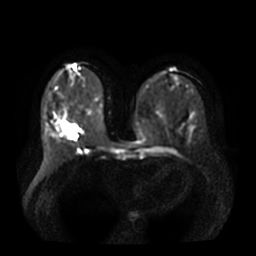
Breast MRI, one axial slice. Slice 15 of 36 in the series (ordered by position). Diffusion-weighted series; image 2 of 4 stored at this slice position (different b-values; order by instance number). 3 T. 5 mm slice thickness. 256 × 256 image matrix. Female patient.
Annotated regions visible in this slice (manually delineated by an expert):
- tumour on diffusion-weighted imaging: bounding box [x1, y1, x2, y2] px = [65, 124, 75, 139]